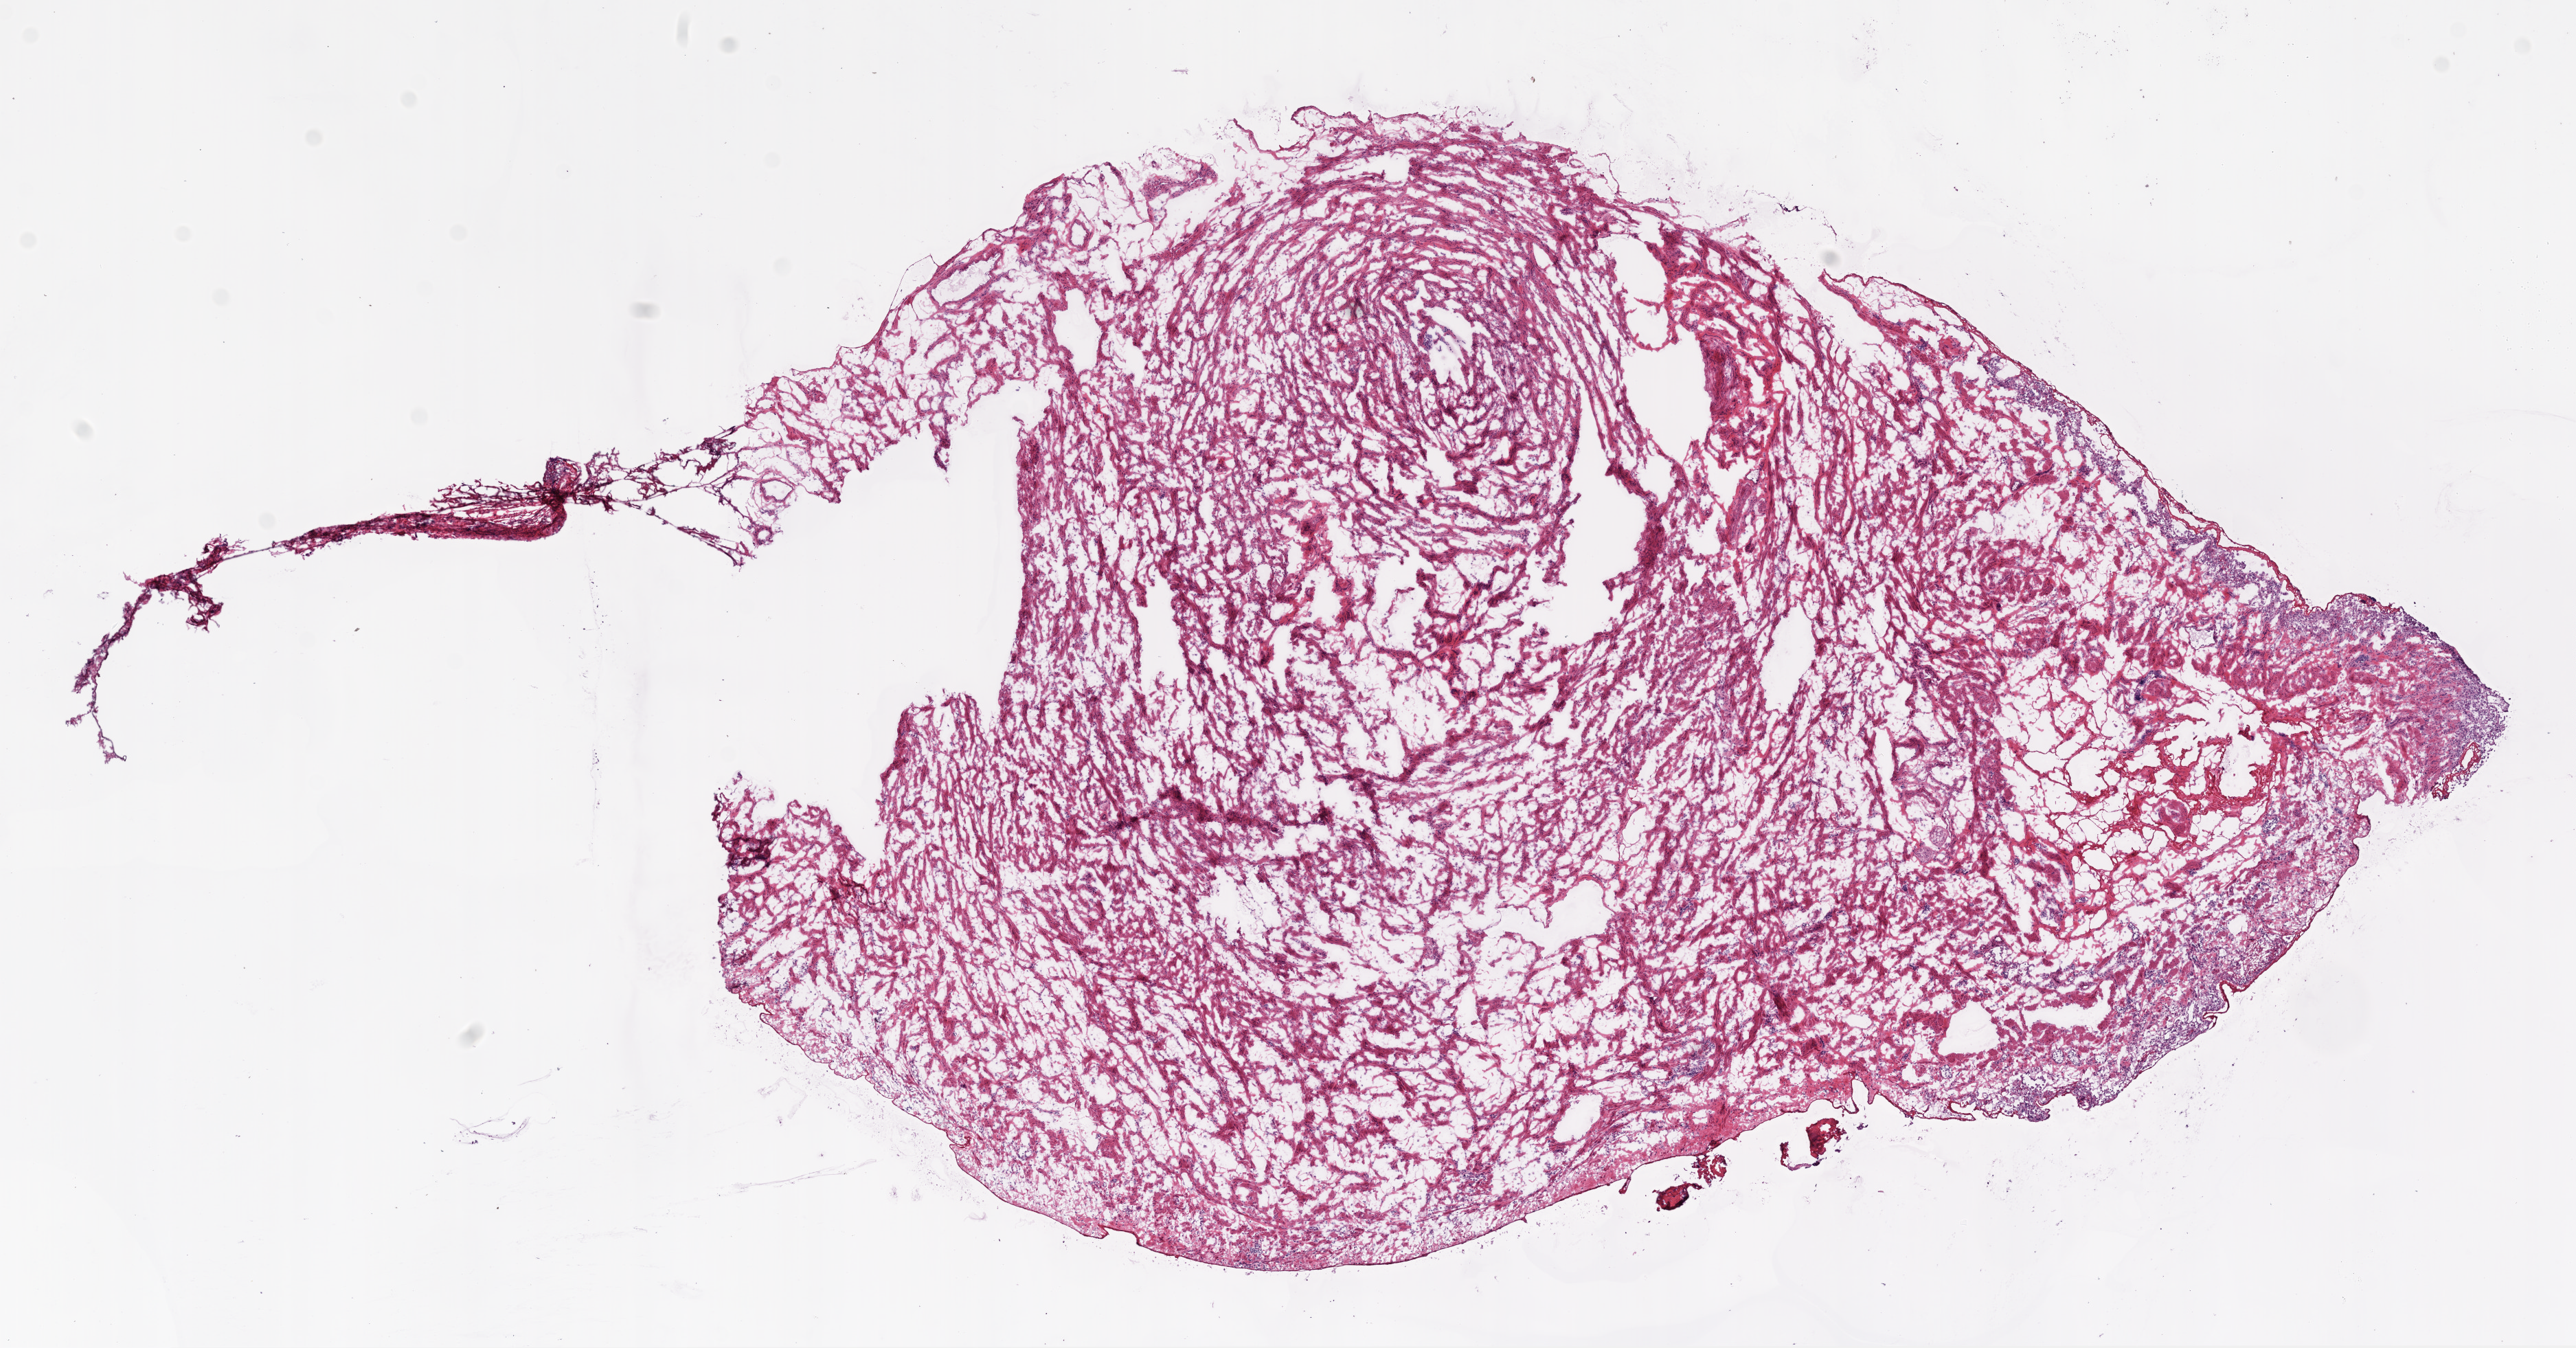
Whole-slide histology image, H&E, shown as a low-resolution overview of the whole scanned area (about 15.0 x 7.9 mm, slide scanned at 20x); frozen section; ovary, solid tissue normal (non-tumour tissue) sample. Female, age 71 years at initial diagnosis.
This section: solid tissue normal sample (biorepository sample class). Patient diagnosis: Serous cystadenocarcinoma, NOS.